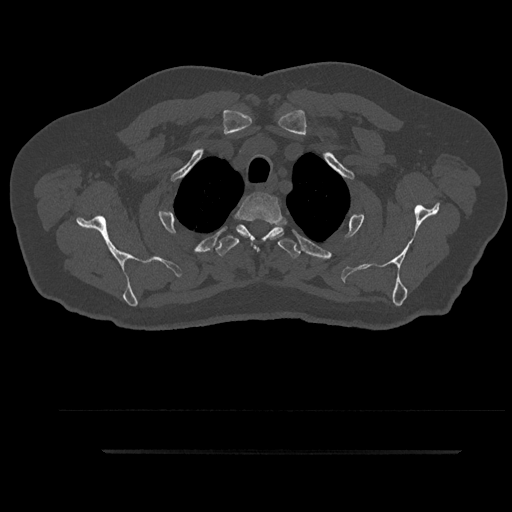
CT including the spine, one axial slice; reconstruction kernel Br40s/3; bone window (W 1800 / L 400 HU); 0.5 mm slice thickness; 512 × 512 image matrix, field of view 432 × 432 mm. Patient: male, 63 years. Case-level facts recorded for this patient, not image findings: primary cancer: renal; vertebrae with lytic lesions (as recorded): T8.
Outlined on this slice (semi-automatically segmented with operator editing):
- T2 vertebra: bounding box (x1, y1, x2, y2) in pixels: (237, 191, 284, 251)
- T3 vertebra: (215, 224, 301, 258)